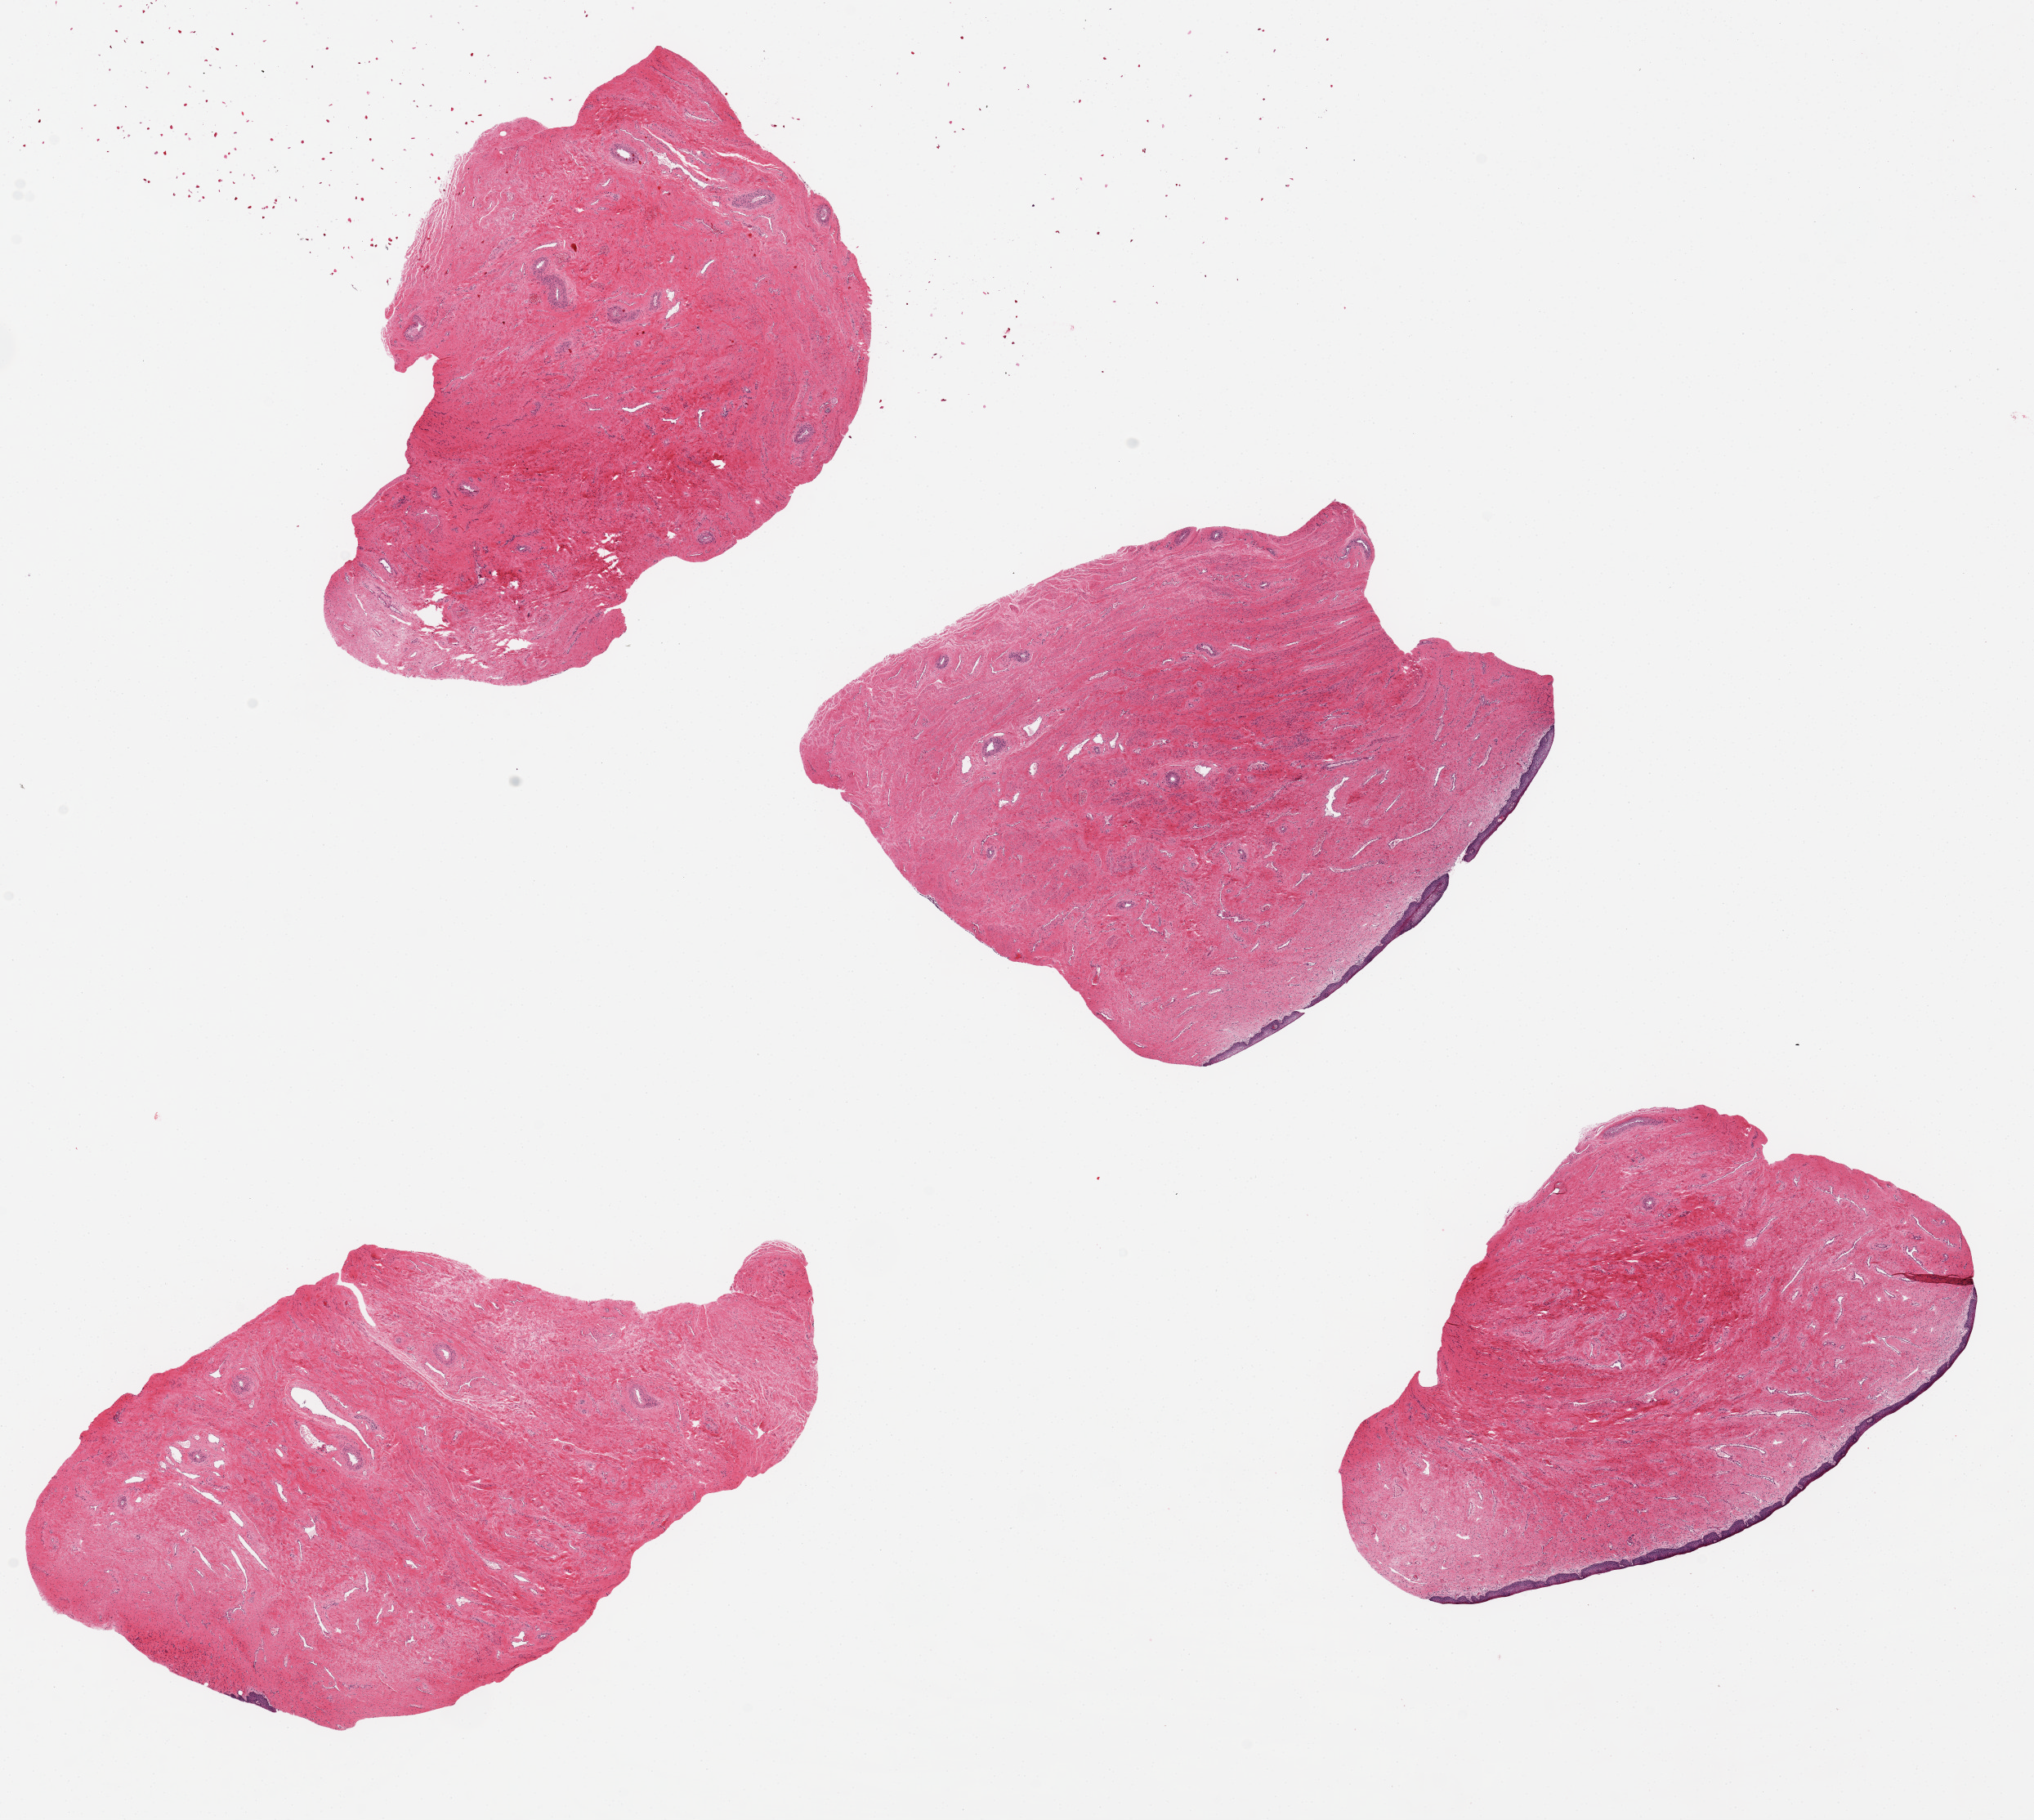
Digitized H&E-stained section, whole scanned area (about 19.7 x 17.6 mm, slide scanned at 20x) shown as a low-resolution overview, PAXgene-fixed, paraffin-embedded tissue, sampled site (target tissue): exocervix, tissue donor sample. Donor sex: female.
- pathologist's review note for this sample: 4 ~6x4mm pieces, 2 with ~ 0.1mm edge of squamous mucosa, 2 with no significant mucosal surface noted